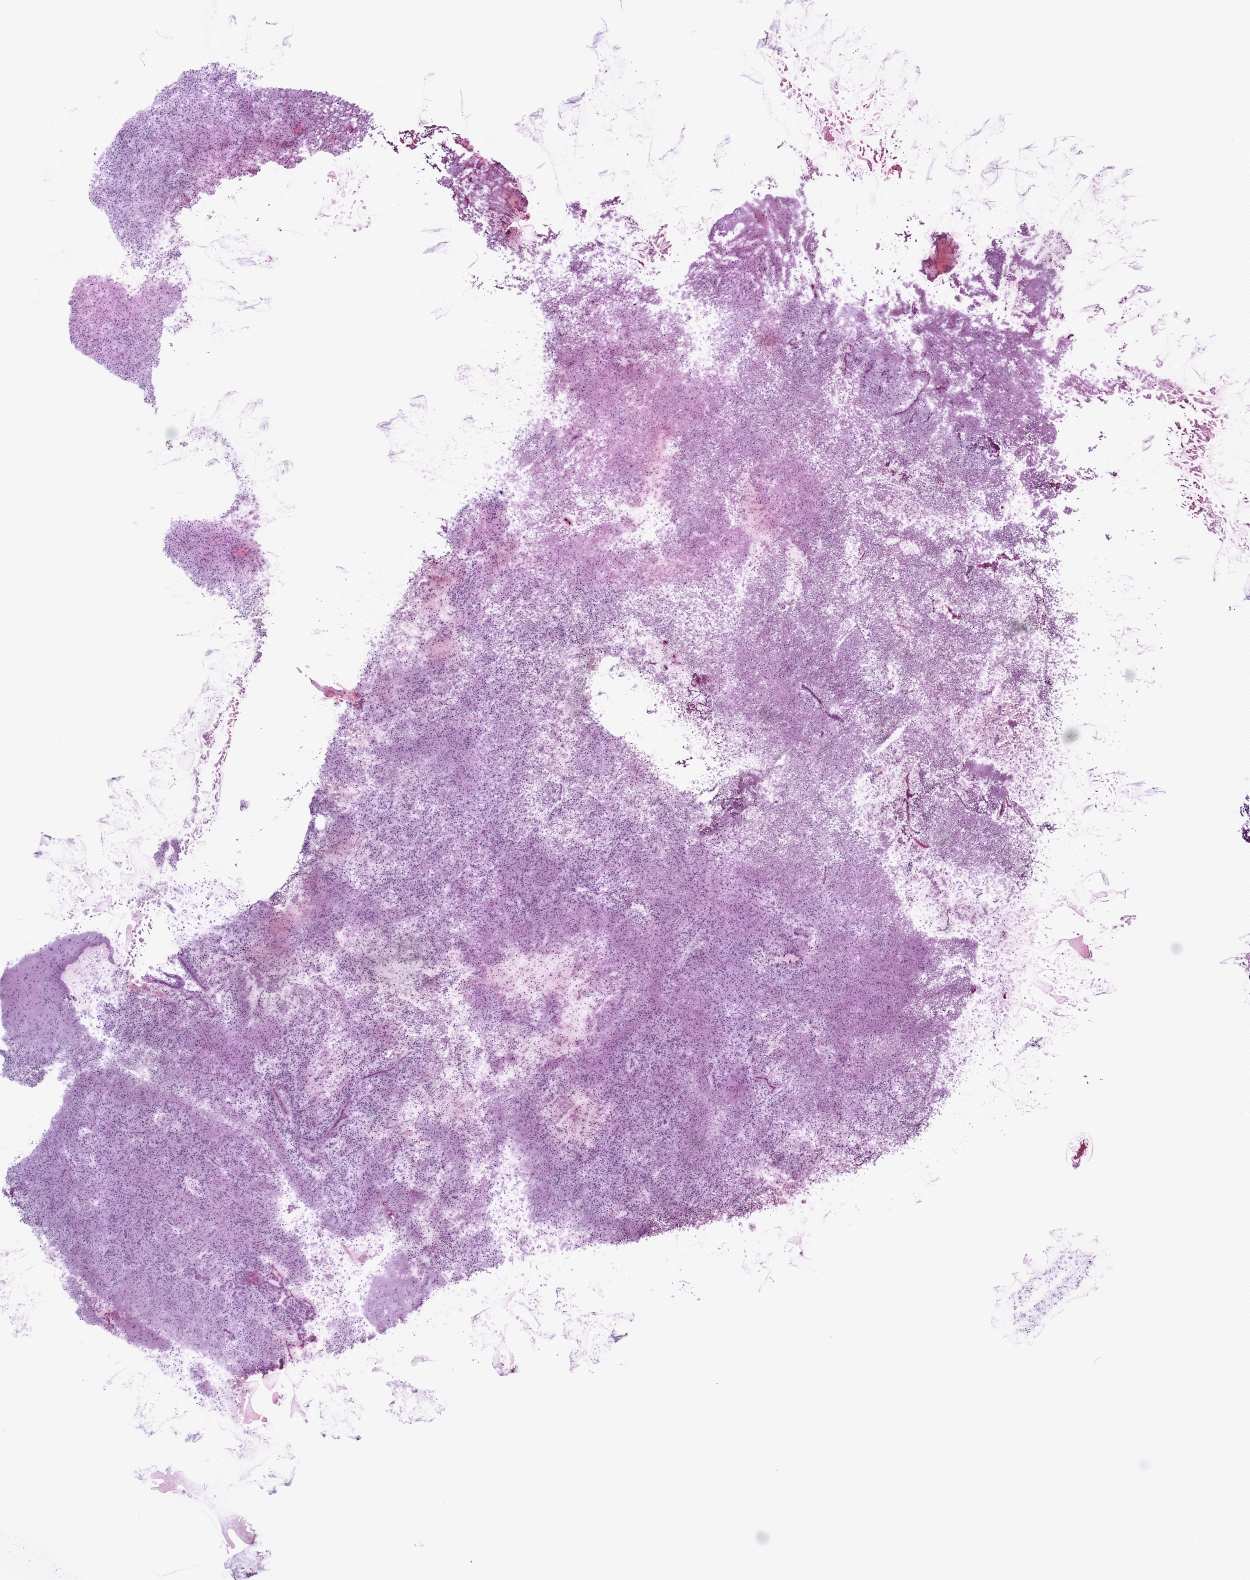
Digitized Hematoxylin and eosin (H&E) stained tissue section (whole slide) — a low-resolution overview of the entire scanned area, about 10.0 x 12.7 mm (acquisition: 20x scan); frozen section from the top of the tissue portion; brain, primary tumour sample. Female patient; age at initial diagnosis 62 years. Composition of this section per pathologist review: tumour cells 85%, tumour nuclei 80%, normal cells 0%, stromal cells 0%, necrosis 15%.
Pathologic diagnosis: Glioblastoma.